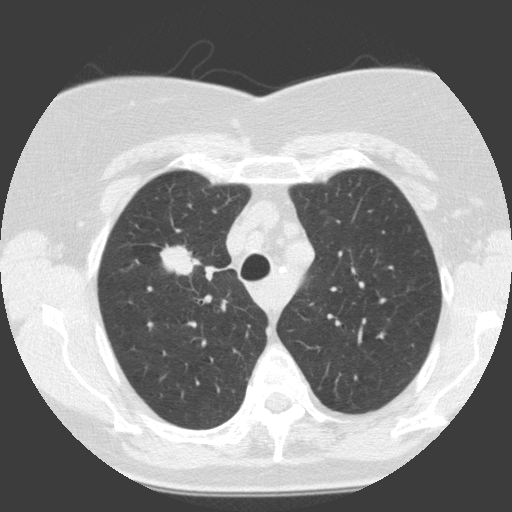
Low-dose screening chest CT, one axial slice. Position 110 of 146 along the scan axis. Lung window (W 1500 / L -600 HU). 512 × 512 image matrix, field of view 300 × 300 mm.
Annotated regions visible in this slice (outlined manually by an expert reader):
- lesion 1 (tumor, upper lobe of right lung): bounding box (x1, y1, x2, y2) in pixels: (160, 245, 194, 276)